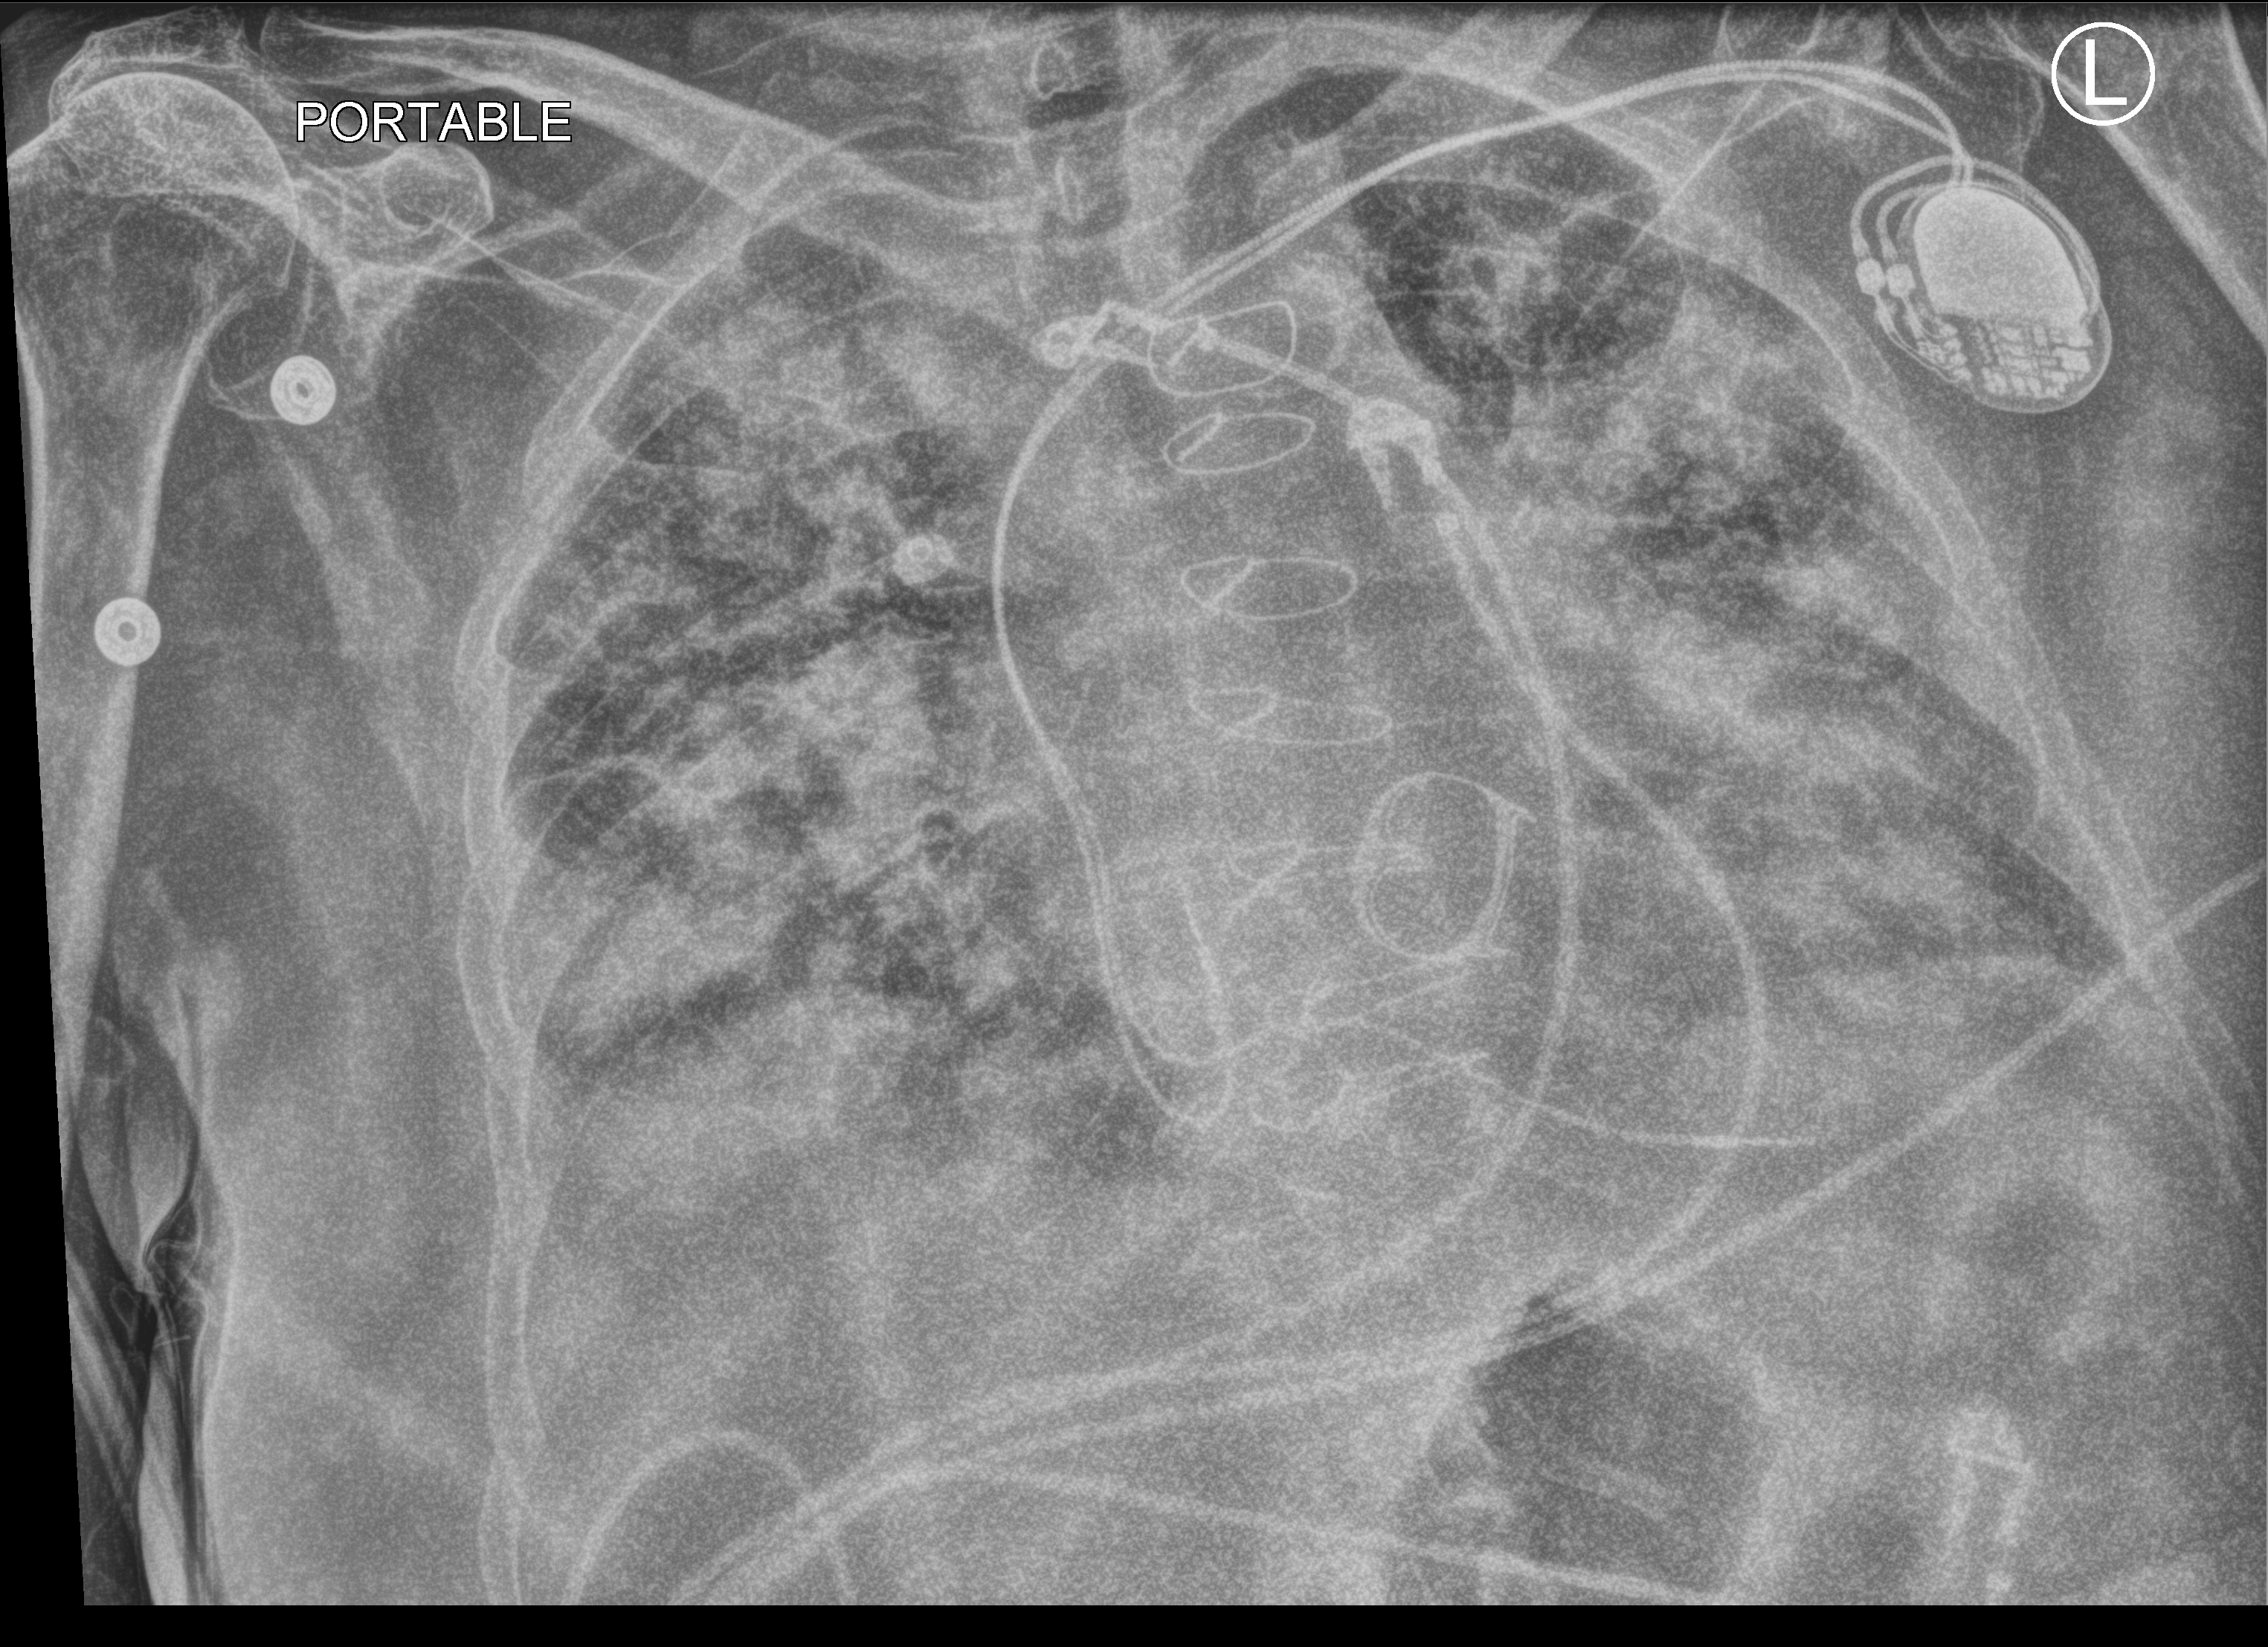
Chest X-ray (portable), anteroposterior (AP) projection. Male patient hospitalised with COVID-19, age 75–90 years.
Hospital-stay facts (about this admission, not read from this image; timing relative to this image not recorded): mechanically ventilated during this hospital stay: no.